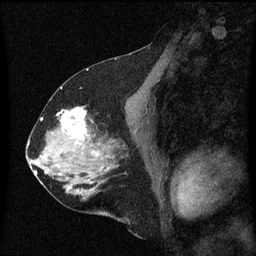
Breast MRI (dynamic contrast-enhanced), one sagittal slice; slice 30 of 60 in the series (ordered by position); dynamic contrast-enhanced series, image 2 of 3 at this slice position (ordered by acquisition); 1.5 T; TE 4.2 ms, TR 8 ms; 2 mm slice thickness; 256 × 256 image matrix, field of view 200 × 200 mm. Patient: female, 58 years.
Structures marked on this image (semi-automatically segmented with operator editing):
- analysis volume of interest (the breast-tissue region the enhancement analysis was run in; not a lesion): bounding box <56,108,99,149> (left, top, right, bottom; pixels)
- tumour enhancement mask (voxels above the 70 % enhancement threshold inside the analysis volume of interest): <62,108,87,139>